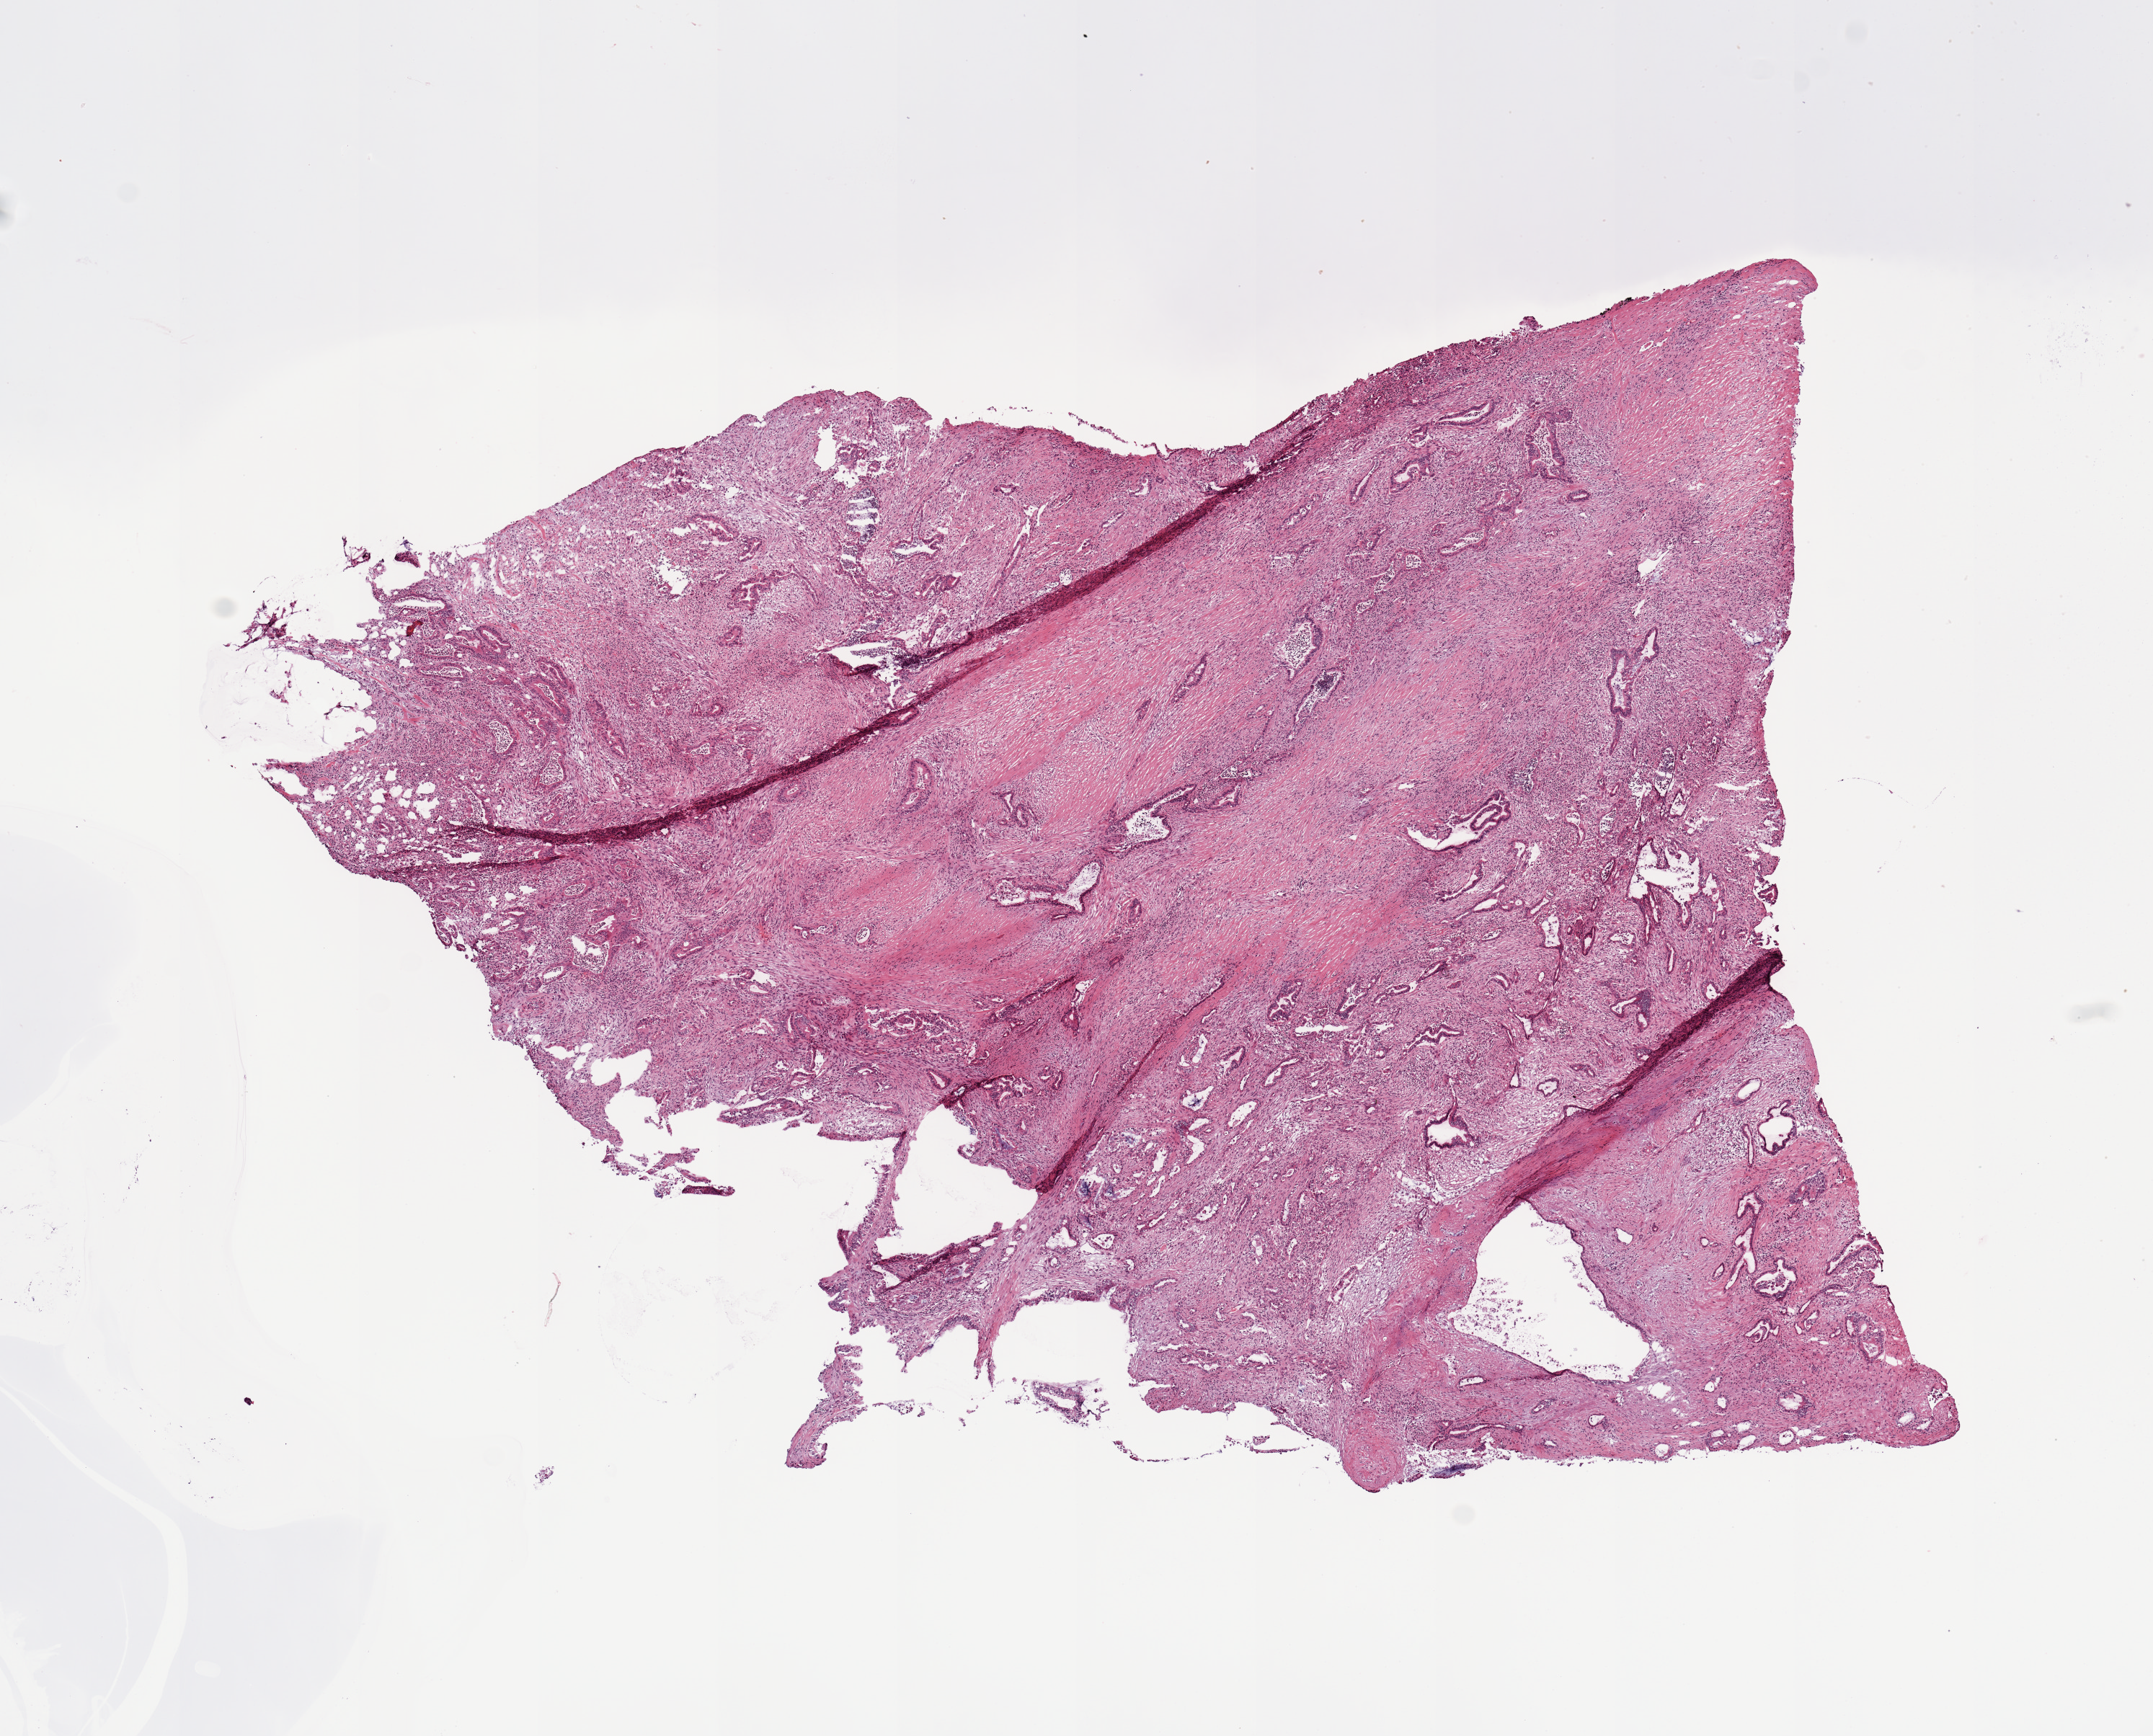
Whole-slide histology image, Hematoxylin and eosin (H&E) stained, shown as a low-resolution overview of the whole scanned area (about 11.8 x 9.5 mm, acquisition: 20x scan), tumour tissue sample, sampled site: pancreas. Female, 59 y/o. Histologic grade: G2 (moderately differentiated). Pathologist review of this section (percent, as recorded): tumour nuclei 40%, necrosis 0%.
* AJCC pathologic stage: IIB
* primary tumour site (as recorded): body
* histologic diagnosis: Infiltrating duct carcinoma, NOS